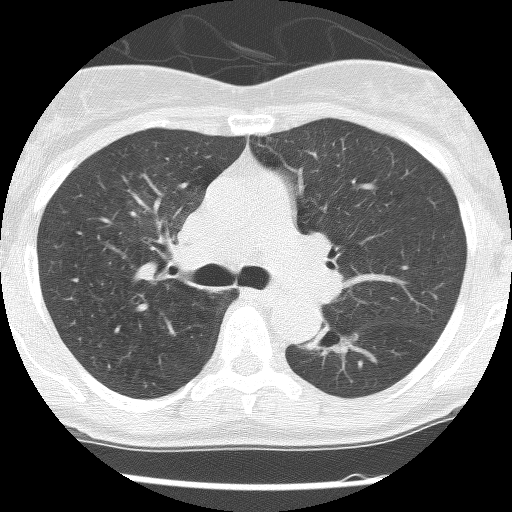
Axial slice from a low-dose chest CT screening exam, second screening round (one year after baseline), lung window (W 1500 / L -600 HU), 2.5 mm slice thickness, lung (sharp) reconstruction kernel (BONE), 120 kVp, 512 × 512 image matrix. Female participant, aged 62 years at enrolment. Former smoker at enrolment.
Lesion marked by an expert reader, bounding box <296,315,350,359> (left, top, right, bottom; pixels). Screening reader's record for this exam (one nodule recorded; not confirmed to be the boxed lesion): non-calcified nodule or mass ≥4 mm, right upper lobe, 30 × 30 mm, poorly defined margins, ground glass attenuation, pre-existing on the prior screen: yes; interval growth: no. Note: the box lies in the patient's left hemithorax on this image, whereas the reader's record names the right lung; they may be different findings. Official screen result: positive, no significant change: stable abnormalities potentially related to lung cancer, unchanged since the prior screening exam. Lung cancer was diagnosed 584 days after this screen (after the third annual screen): squamous cell carcinoma, NOS, left lower lobe, stage IIIB (AJCC 6th edition), 31 mm at pathology.